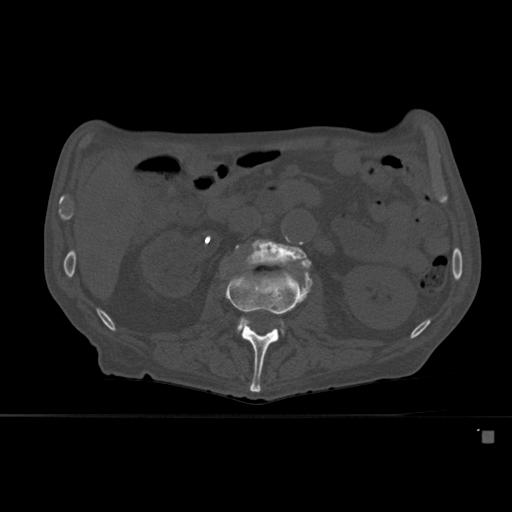
CT including the spine, one axial slice. Slice 229 of 527 in the series (ordered by position). Bone window (W 1800 / L 400 HU). 512 × 512 image matrix. Patient: male, 78 years. From the clinical record (not read from this slice): primary cancer: prostate.
Outlined on this slice (semi-automatically segmented with operator editing):
- L2 vertebra: box from (x=225, y=266) to (x=312, y=392) px
- L3 vertebra: (x=236, y=236)–(x=312, y=330)